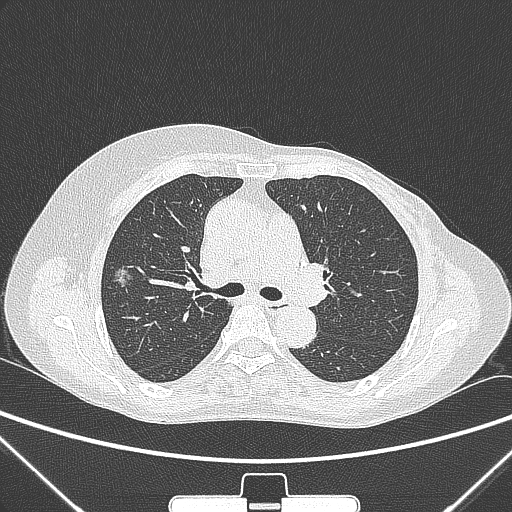
Chest CT, one axial slice. Slice 161 of 265 in the series (ordered by position). 120 kVp. Lung window (W 1500 / L -600 HU). 512 × 512 image matrix, field of view 350 × 350 mm. Patient: female, 64 years. From the clinical record (not read from this slice): clinical TNM (as recorded): T1c N0 M0.
Annotated regions visible in this slice (bounding box drawn by a radiologist):
- lung tumour (recorded histology: adenocarcinoma): bounding box [x1, y1, x2, y2] px = [104, 257, 140, 293]